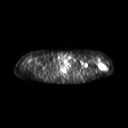
FDG PET of an extremity soft-tissue mass (from a PET/CT study), one axial slice. Position 207 of 267 along the scan axis. 3.27 mm slice thickness. 128 × 128 image matrix. Female patient, age 28 years. Case-level facts recorded for this patient, not image findings: histological type: malignant fibrous histiocytoma; grade: low; site of the primary tumour: left arm.
Outlined on this slice (expert contour drawn on MRI and transferred to this co-registered scan by the dataset authors):
- gross tumour volume (mass): bounding box [x1, y1, x2, y2] px = [98, 62, 107, 70]